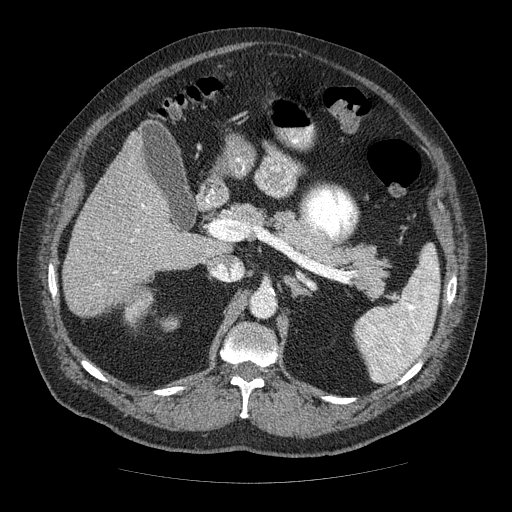
Contrast-enhanced abdominal CT (liver protocol), one axial slice; slice 27 of 85 in the series (ordered by position); reconstruction kernel STANDARD; soft-tissue window (W 400 / L 40 HU); 512 × 512 image matrix, field of view 420 × 420 mm. Case-level facts recorded for this patient, not image findings: diagnosis: hepatocellular carcinoma (patient treated with transarterial chemoembolisation; whether this scan precedes or follows treatment is not stated here); TNM stage (as recorded): Stage-IIIA; Child-Pugh class: A; tumour nodularity: multinodular.
Outlined on this slice (semi-automatically segmented with operator editing):
- liver parenchyma outside the tumour (the mass and vessels are separate outlines, so this box may not span the whole liver): bounding box (x1, y1, x2, y2) in pixels: (62, 130, 212, 316)
- mass: (125, 295, 149, 320)
- liver vessels: (98, 204, 209, 285)